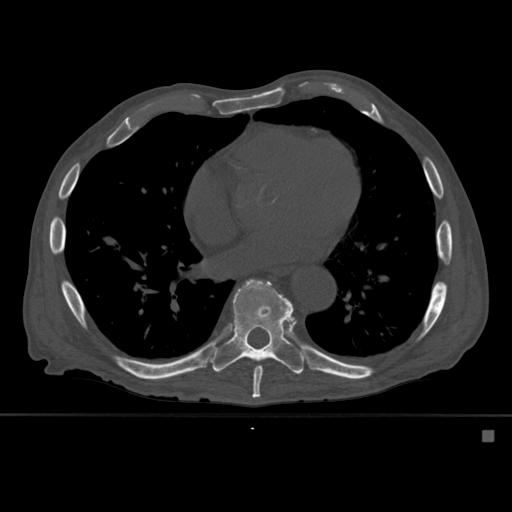
CT including the spine, one axial slice. Slice 338 of 527 in the series (ordered by position). Bone window (W 1800 / L 400 HU). 1.5 mm slice thickness. 512 × 512 image matrix, field of view 373 × 373 mm. Male patient, age 78 years. Case-level facts recorded for this patient, not image findings: primary cancer: prostate.
Outlined on this slice (semi-automatically segmented with operator editing):
- T8 vertebra: bounding box (x1, y1, x2, y2) in pixels: (252, 366, 262, 398)
- T9 vertebra: (213, 279, 305, 385)